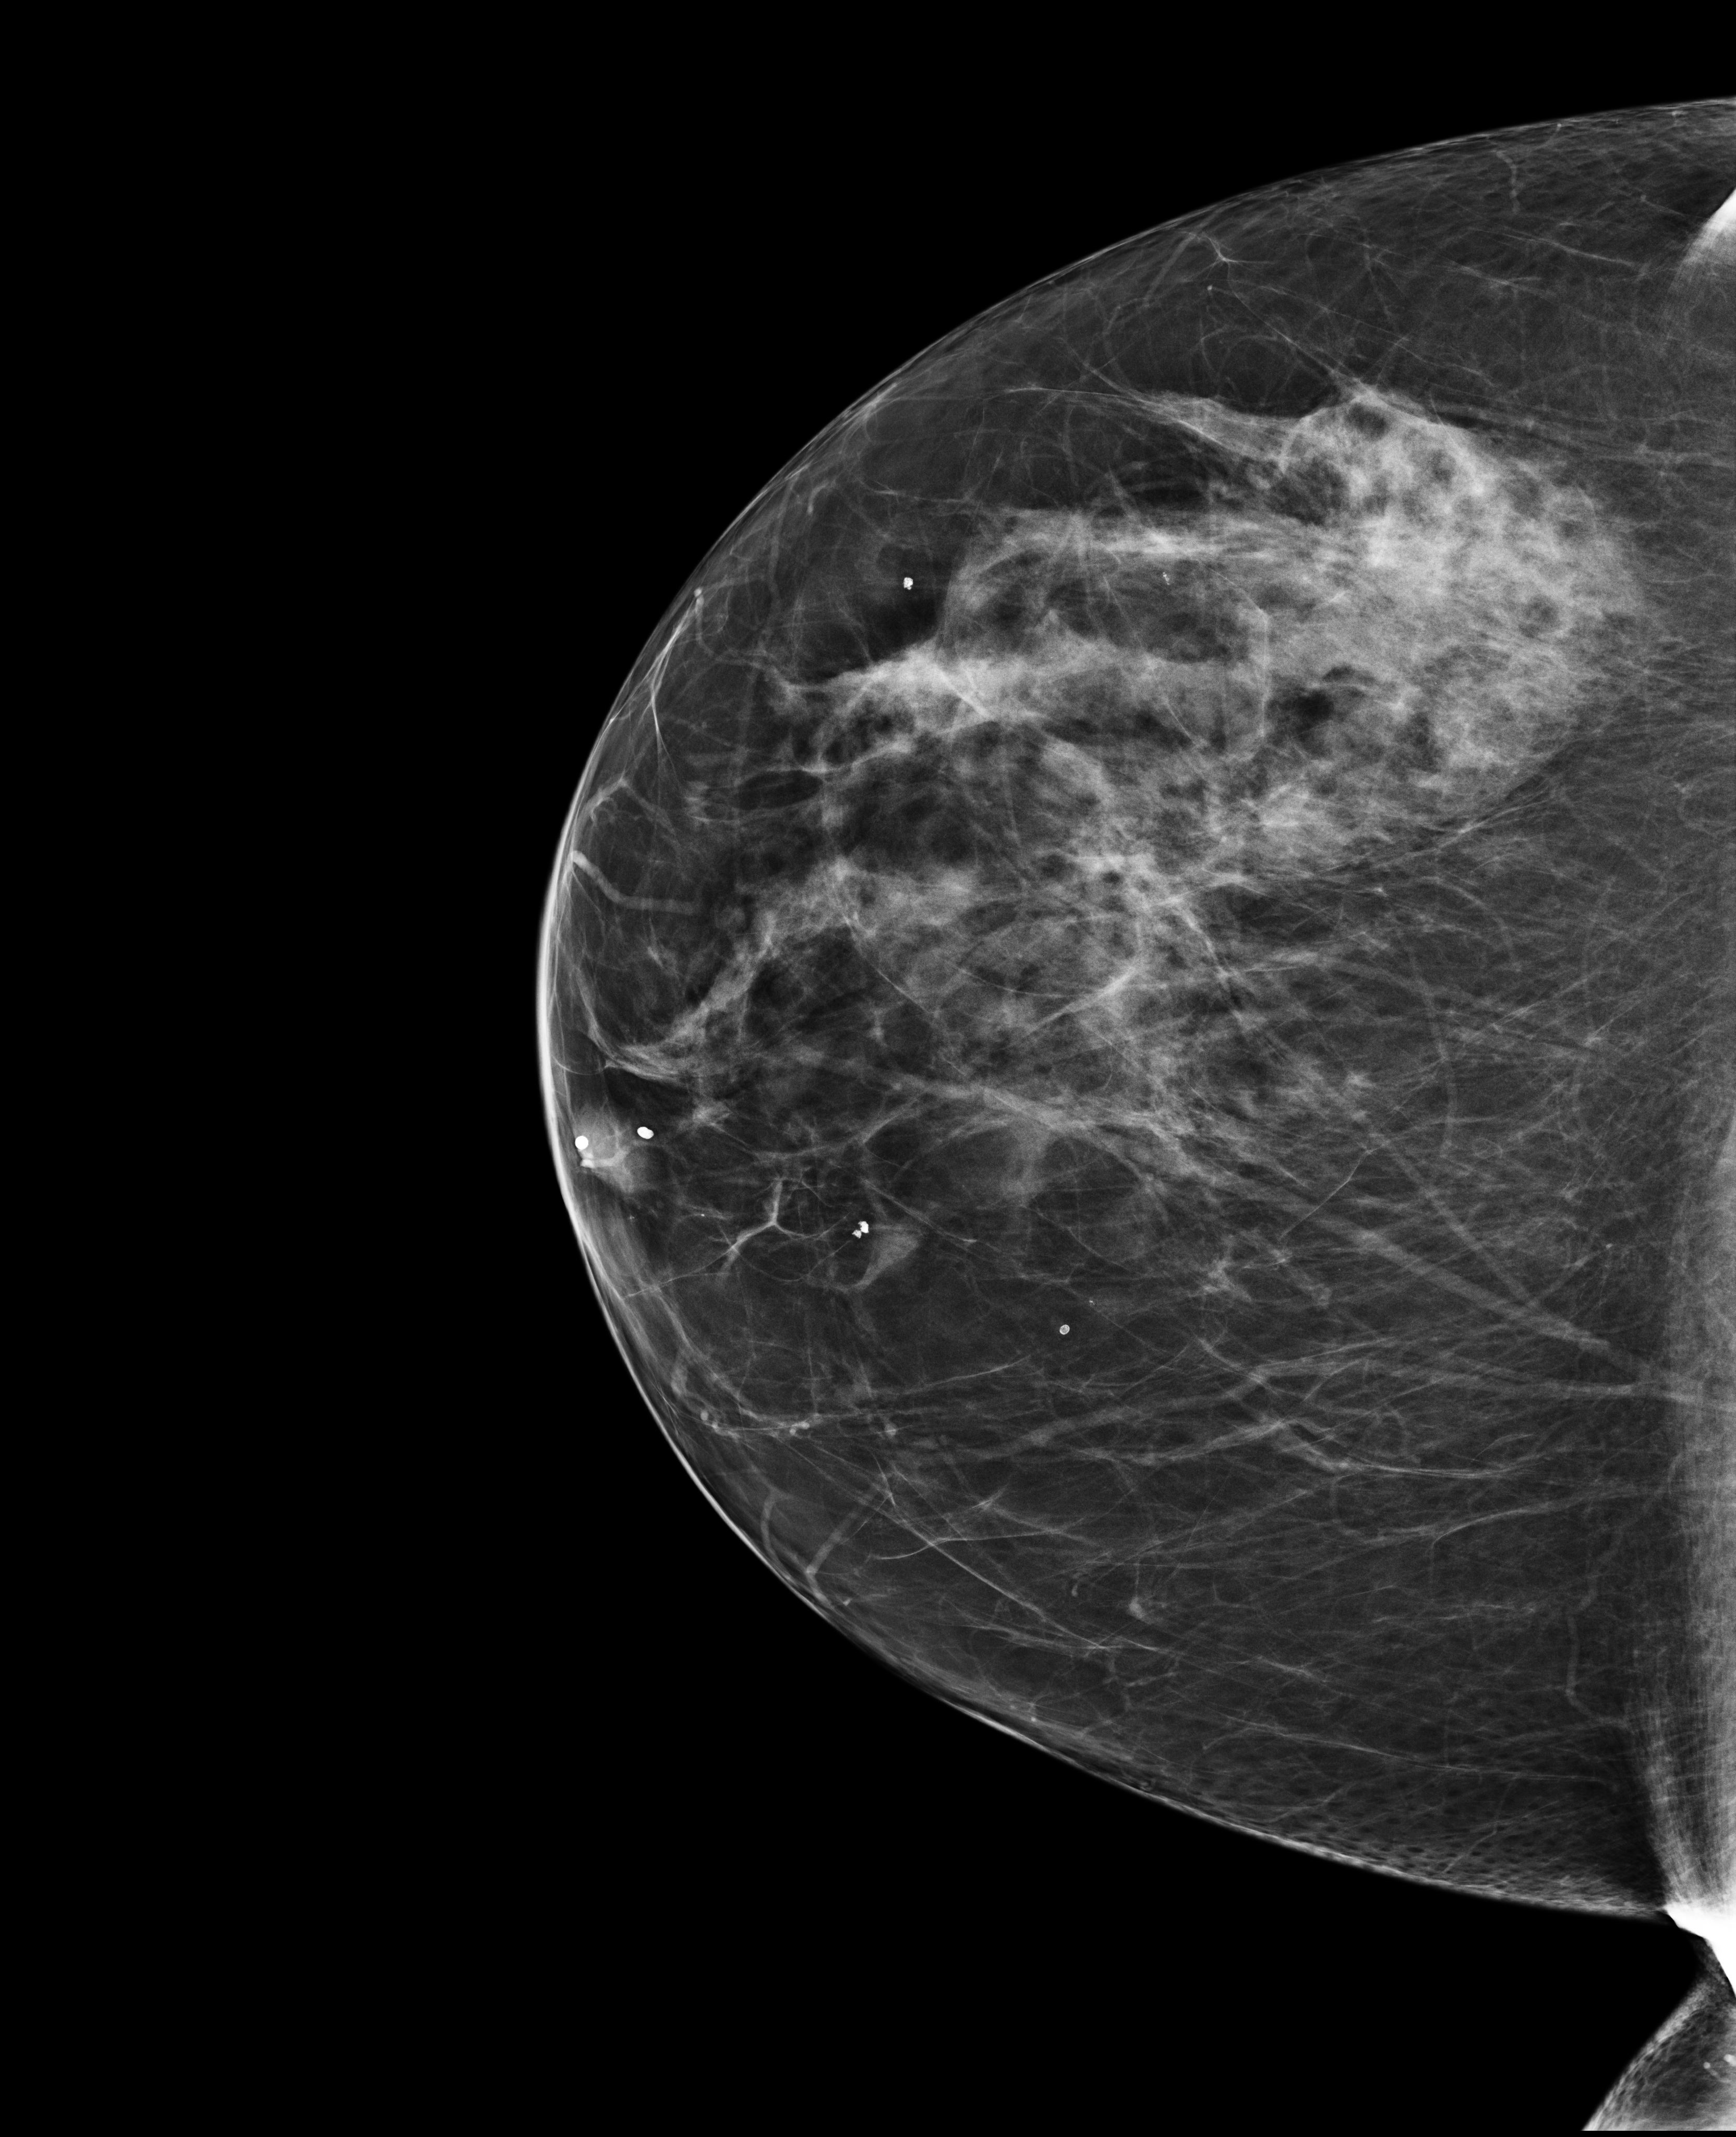
Annual screening mammography examination. Patient aged 61 years (female).
Image type: full-field digital mammogram. Breast: right. Projection: CC view.